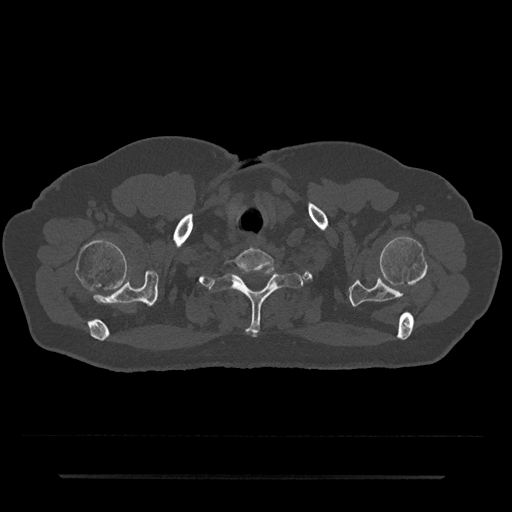
CT including the spine, one axial slice. Position 649 of 797 along the scan axis. Reconstruction kernel Br40s/3. 120 kVp. Bone window (W 1800 / L 400 HU). 0.5 mm slice thickness. 512 × 512 image matrix, field of view 437 × 437 mm. Male patient, age 69 years. Case-level facts recorded for this patient, not image findings: primary cancer: prostate.
Outlined on this slice (semi-automatically segmented with operator editing):
- T1 vertebra: bounding box <209,267,304,335> (left, top, right, bottom; pixels)